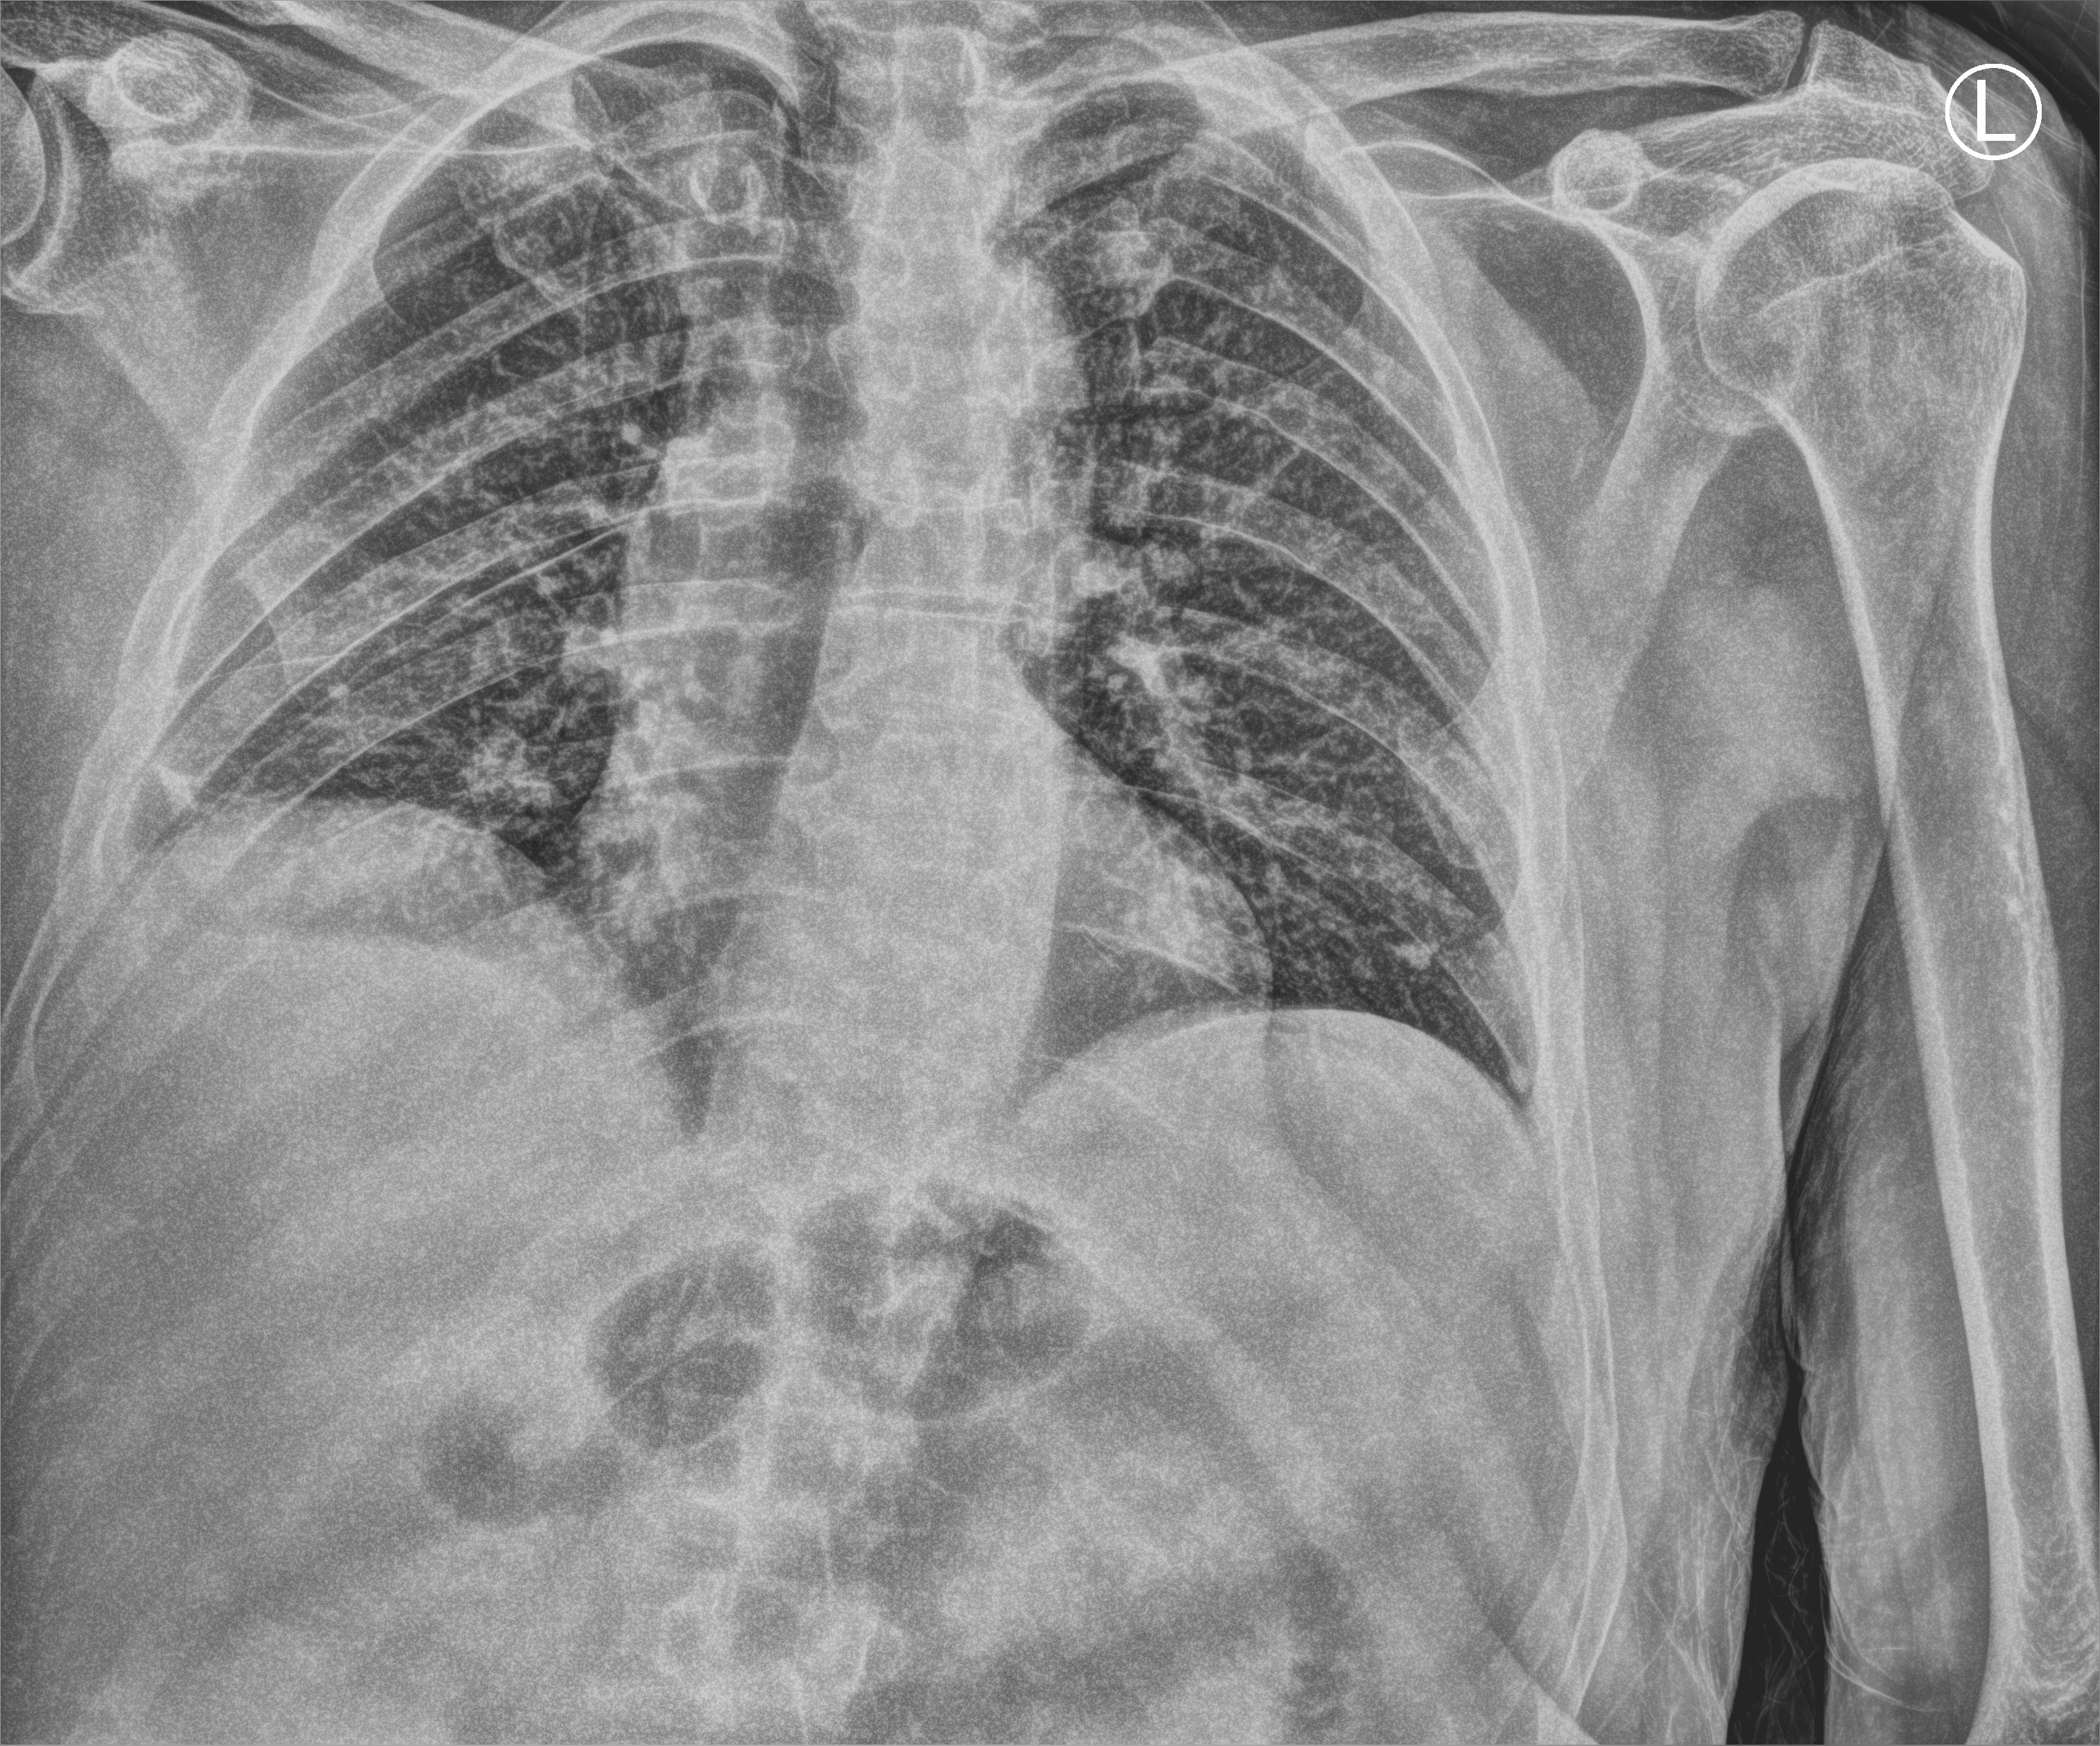
Portable chest radiograph; anteroposterior (AP) projection. Male patient hospitalised with COVID-19, age 75–90 years.
Hospital-stay facts (about this admission, not read from this image; timing relative to this image not recorded):
- smoking status (admission record): never
- length of hospital stay: 7 days